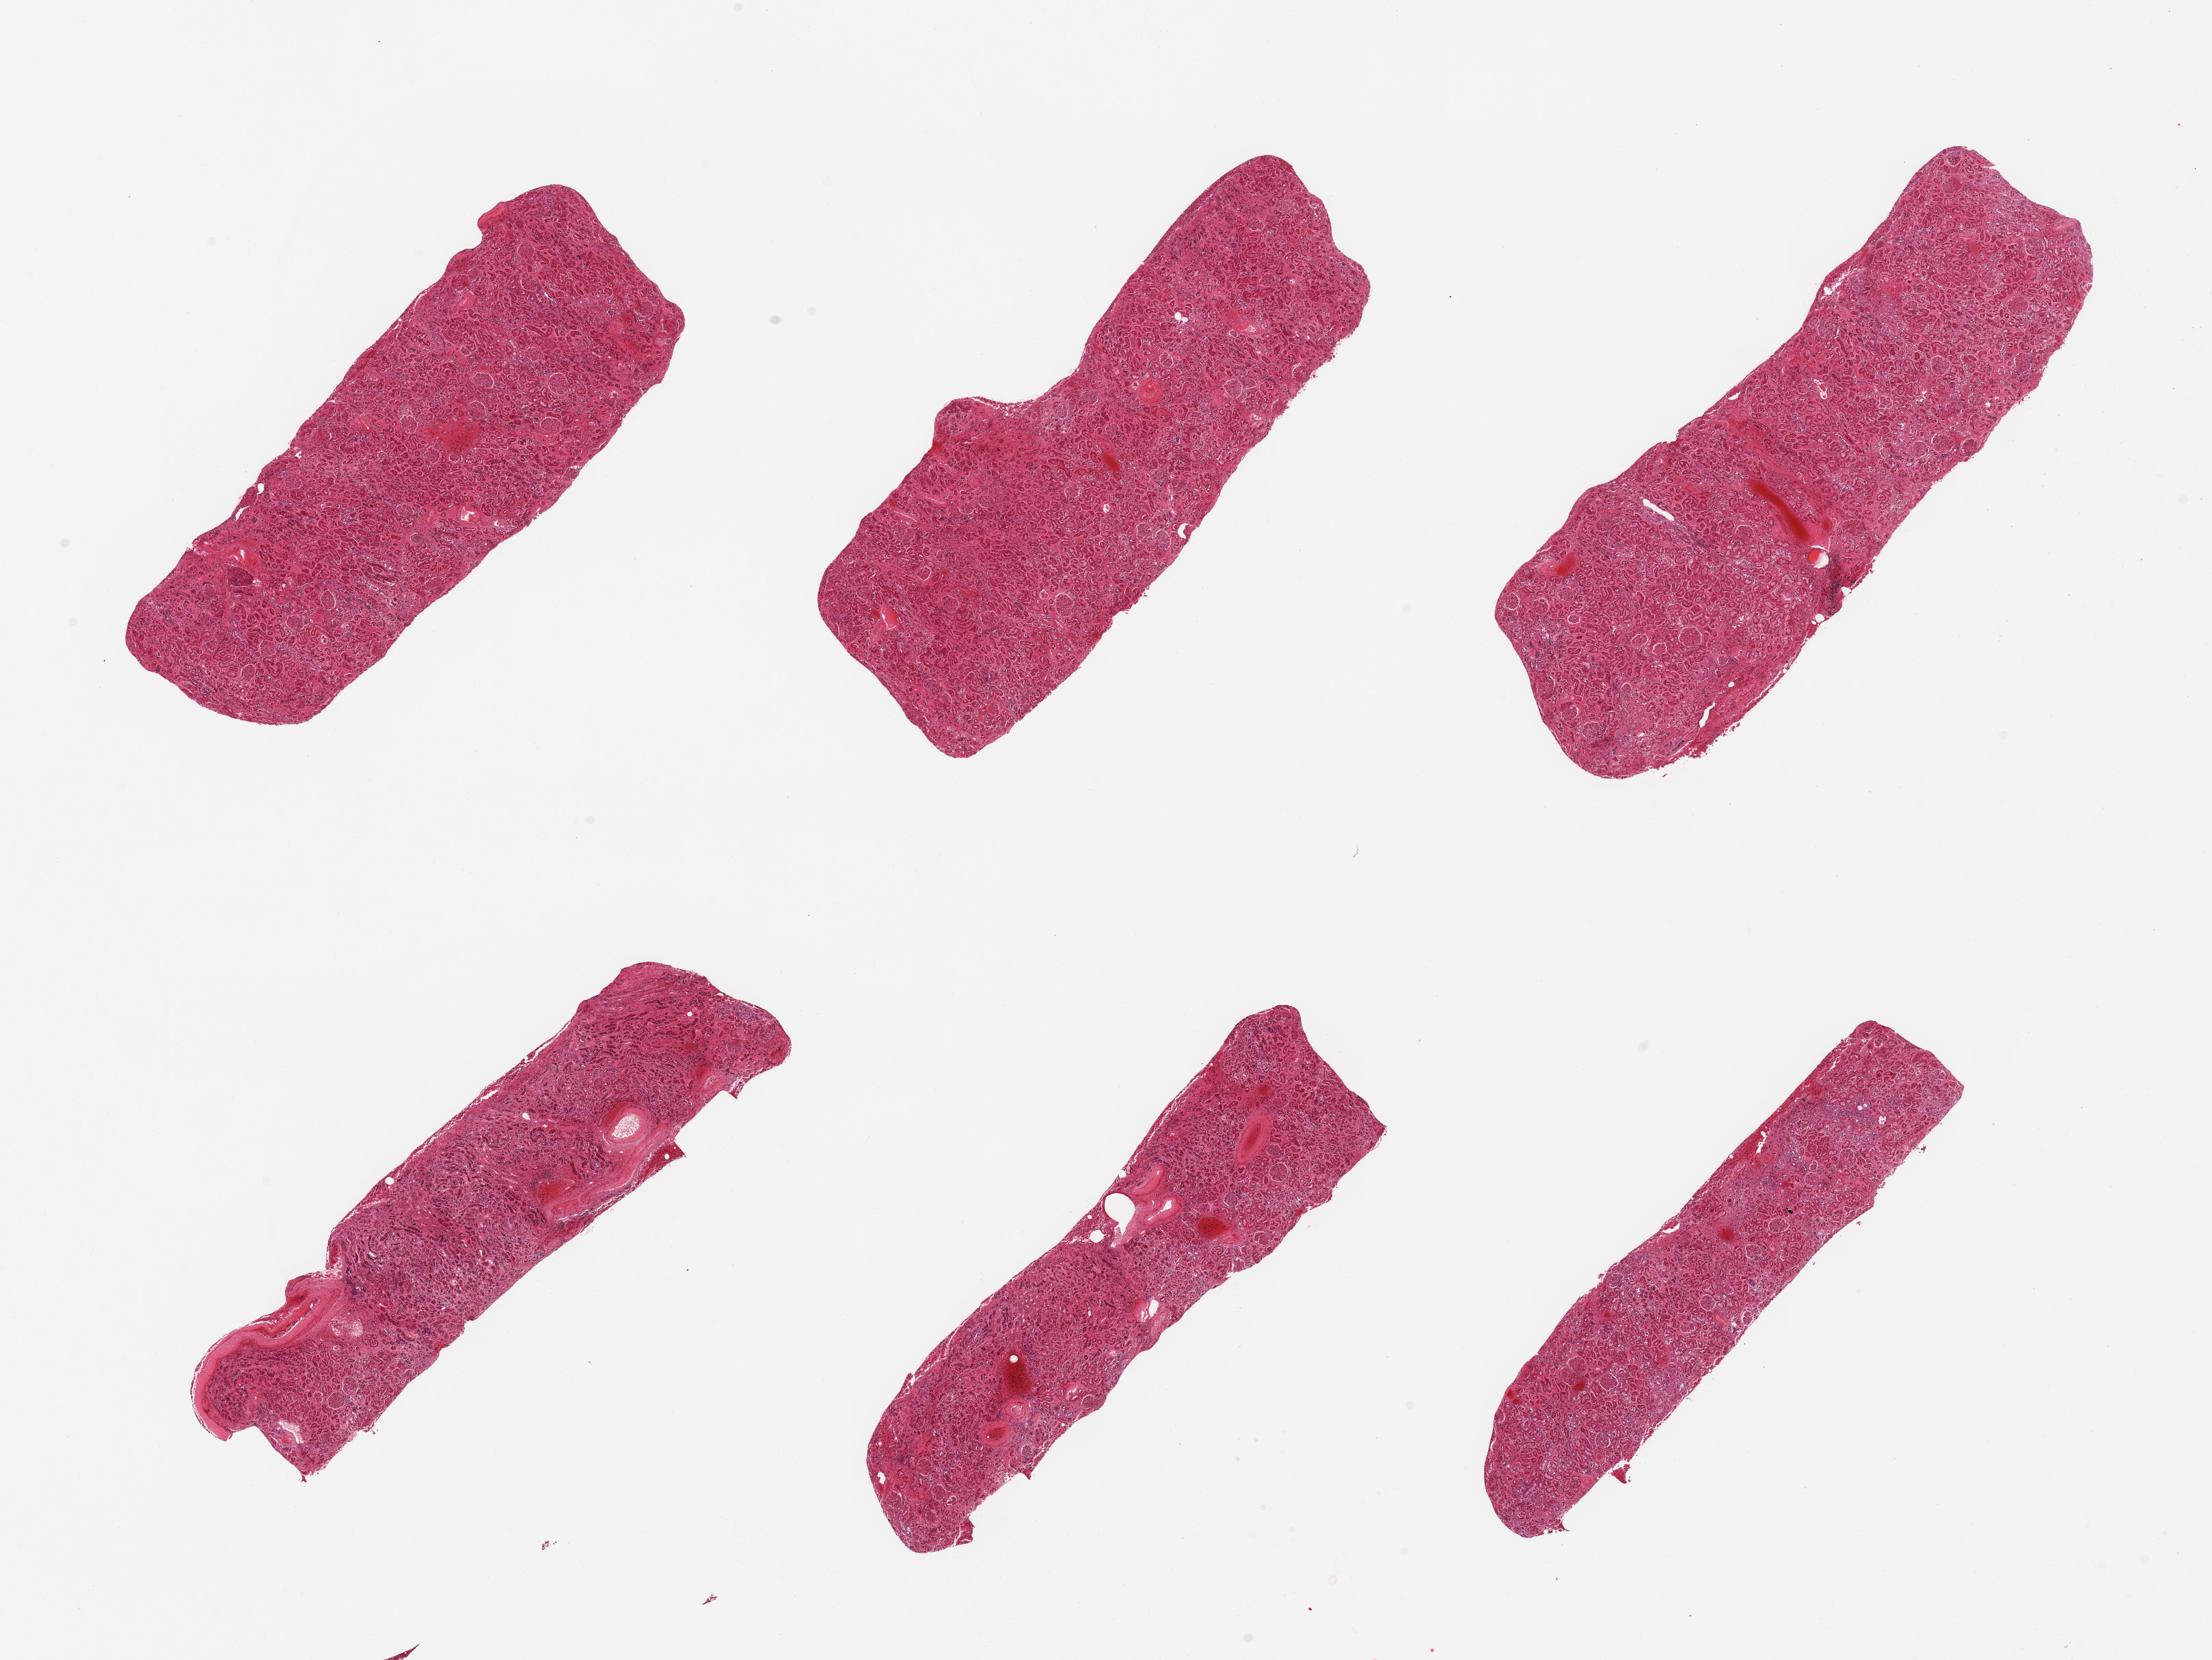
Digitized haematoxylin and eosin-stained section — shown as a low-resolution overview of the whole scanned area (about 25.6 x 19.2 mm, from a 20x scan). PAXgene-fixed, paraffin-embedded tissue. Target tissue: renal cortex. Donor tissue sample. Male donor.
Review note (as recorded): 6 pieces, glomeruli present in all sections, which show advanced autolysis.